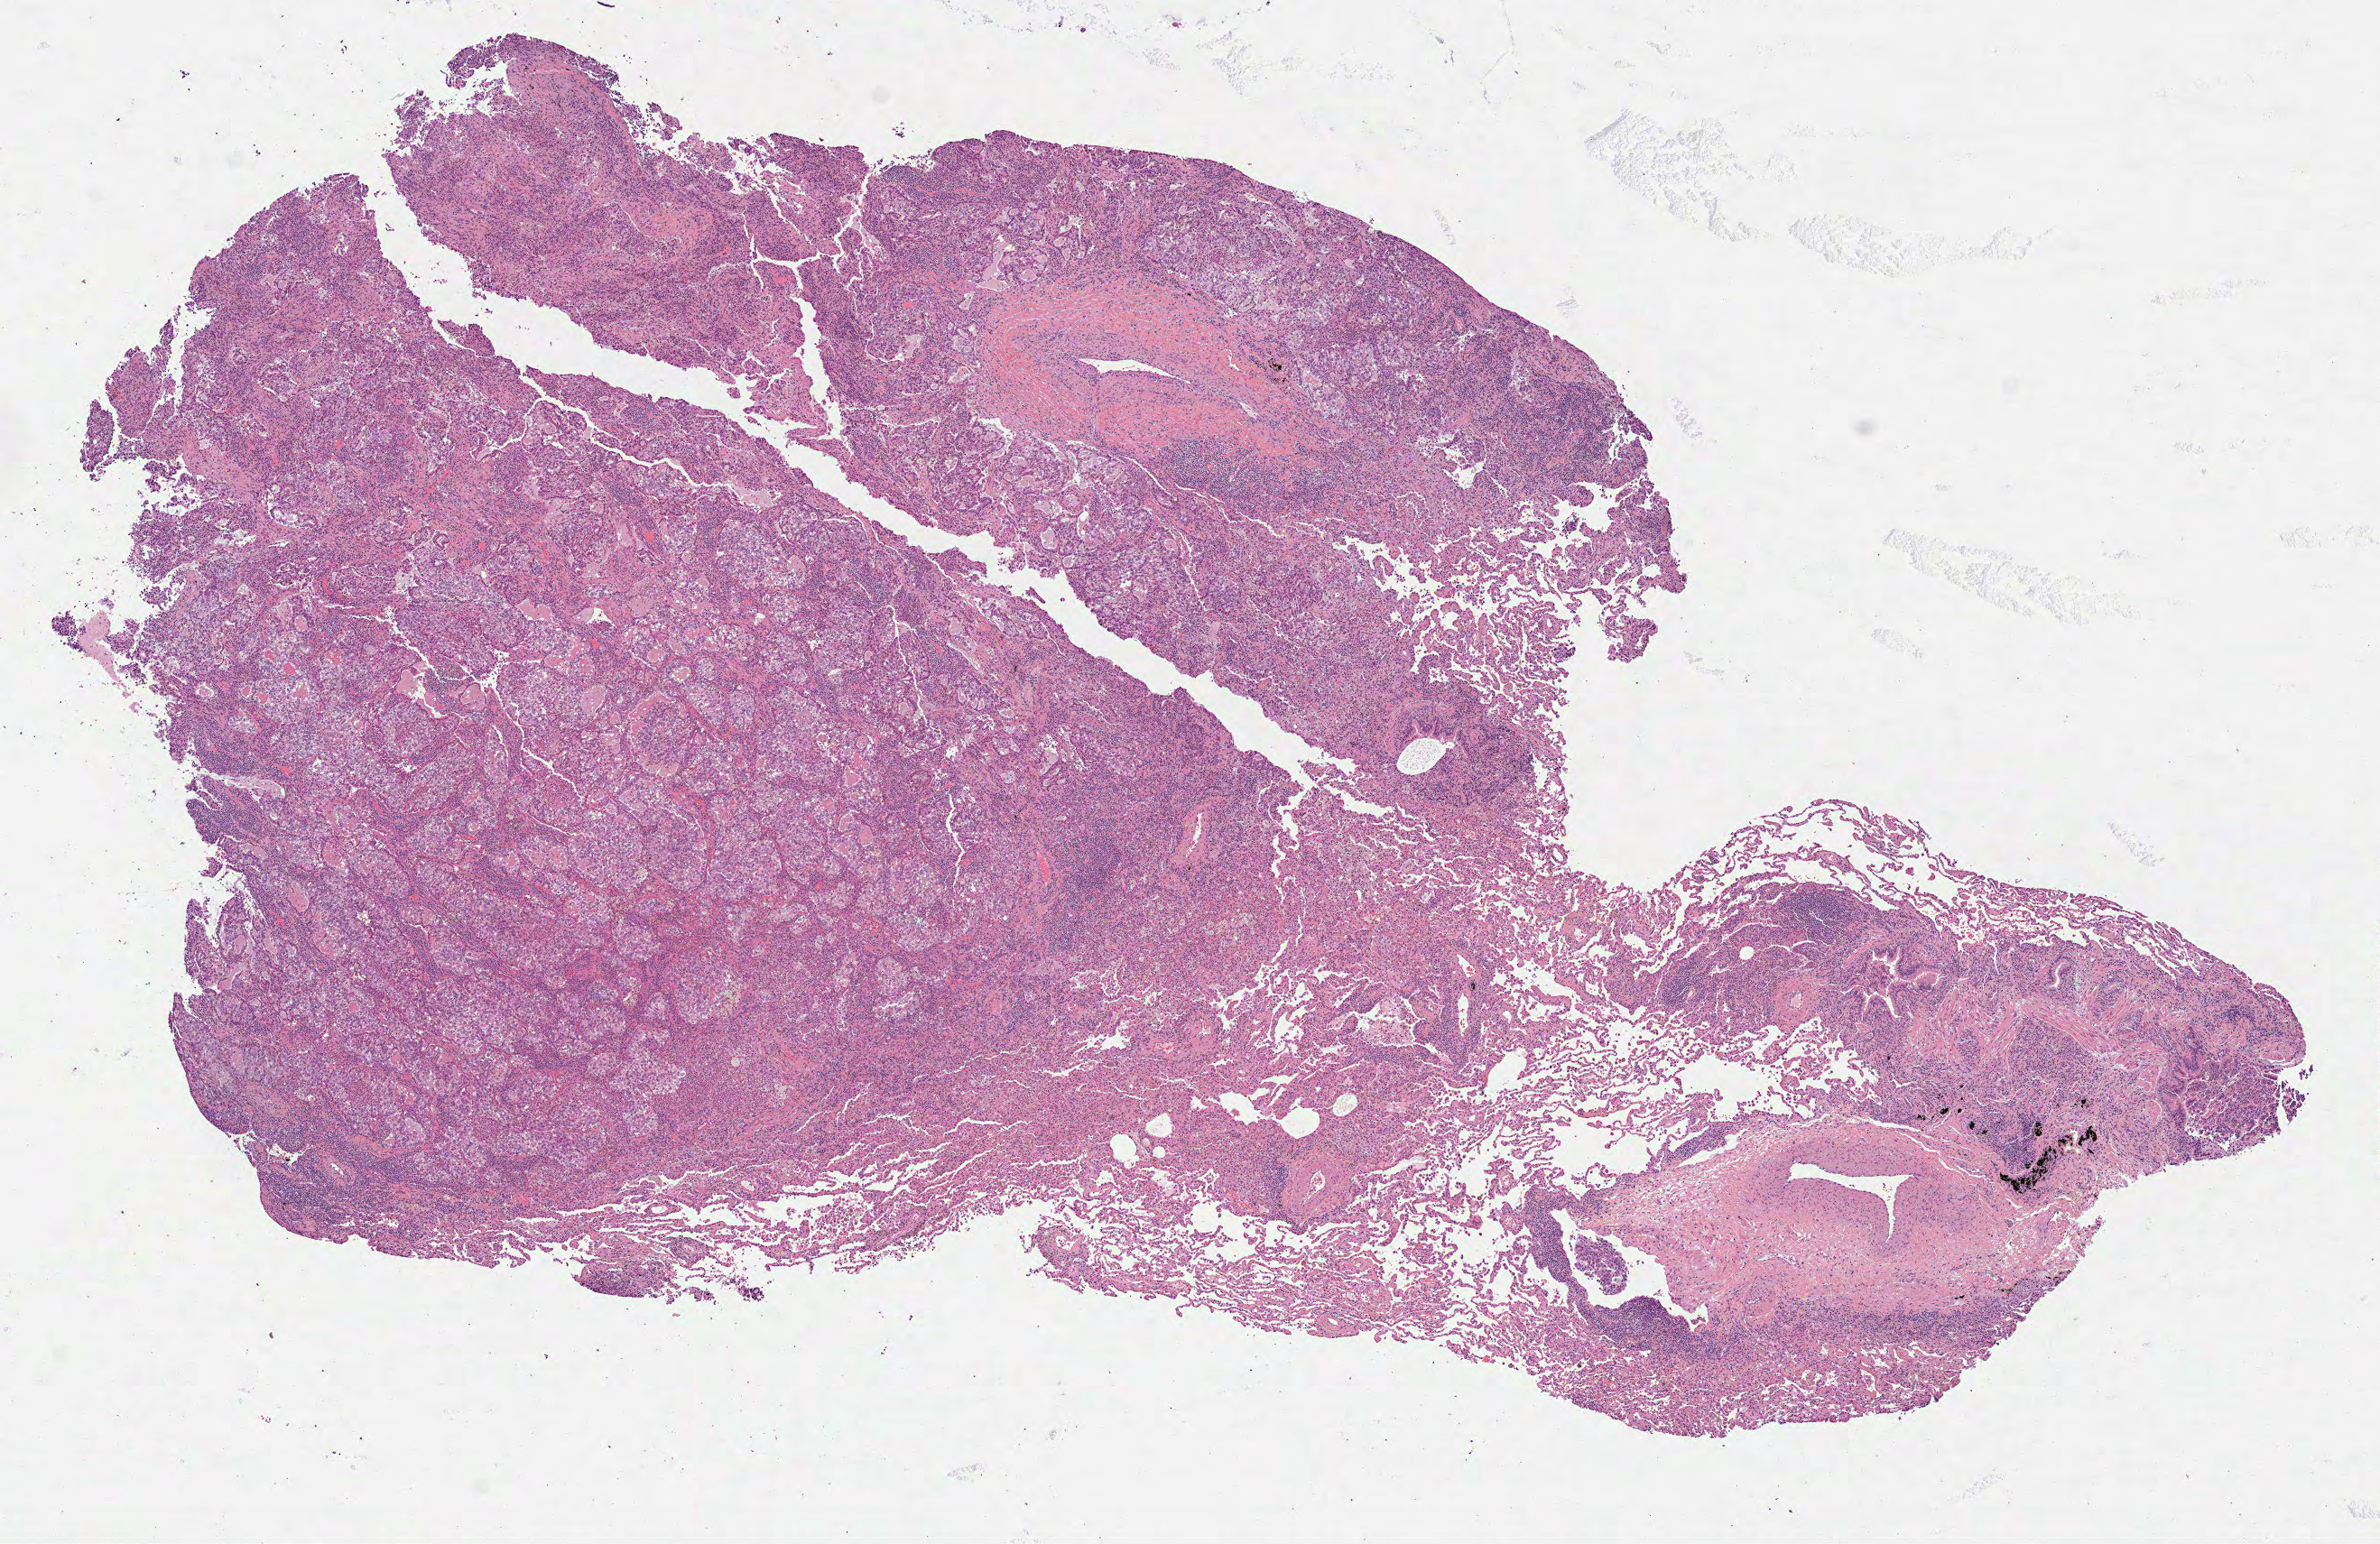
Whole-slide histology image, H&E-stained, shown as a low-resolution overview of the whole scanned area (about 10.6 x 6.9 mm), FFPE section, primary tumour sample from the lung. Female patient; age at initial diagnosis 59 years.
TNM: T2 N0 MX. Diagnosis: Adenocarcinoma, NOS (lower lobe, lung). AJCC pathologic stage: IB (7th edition).